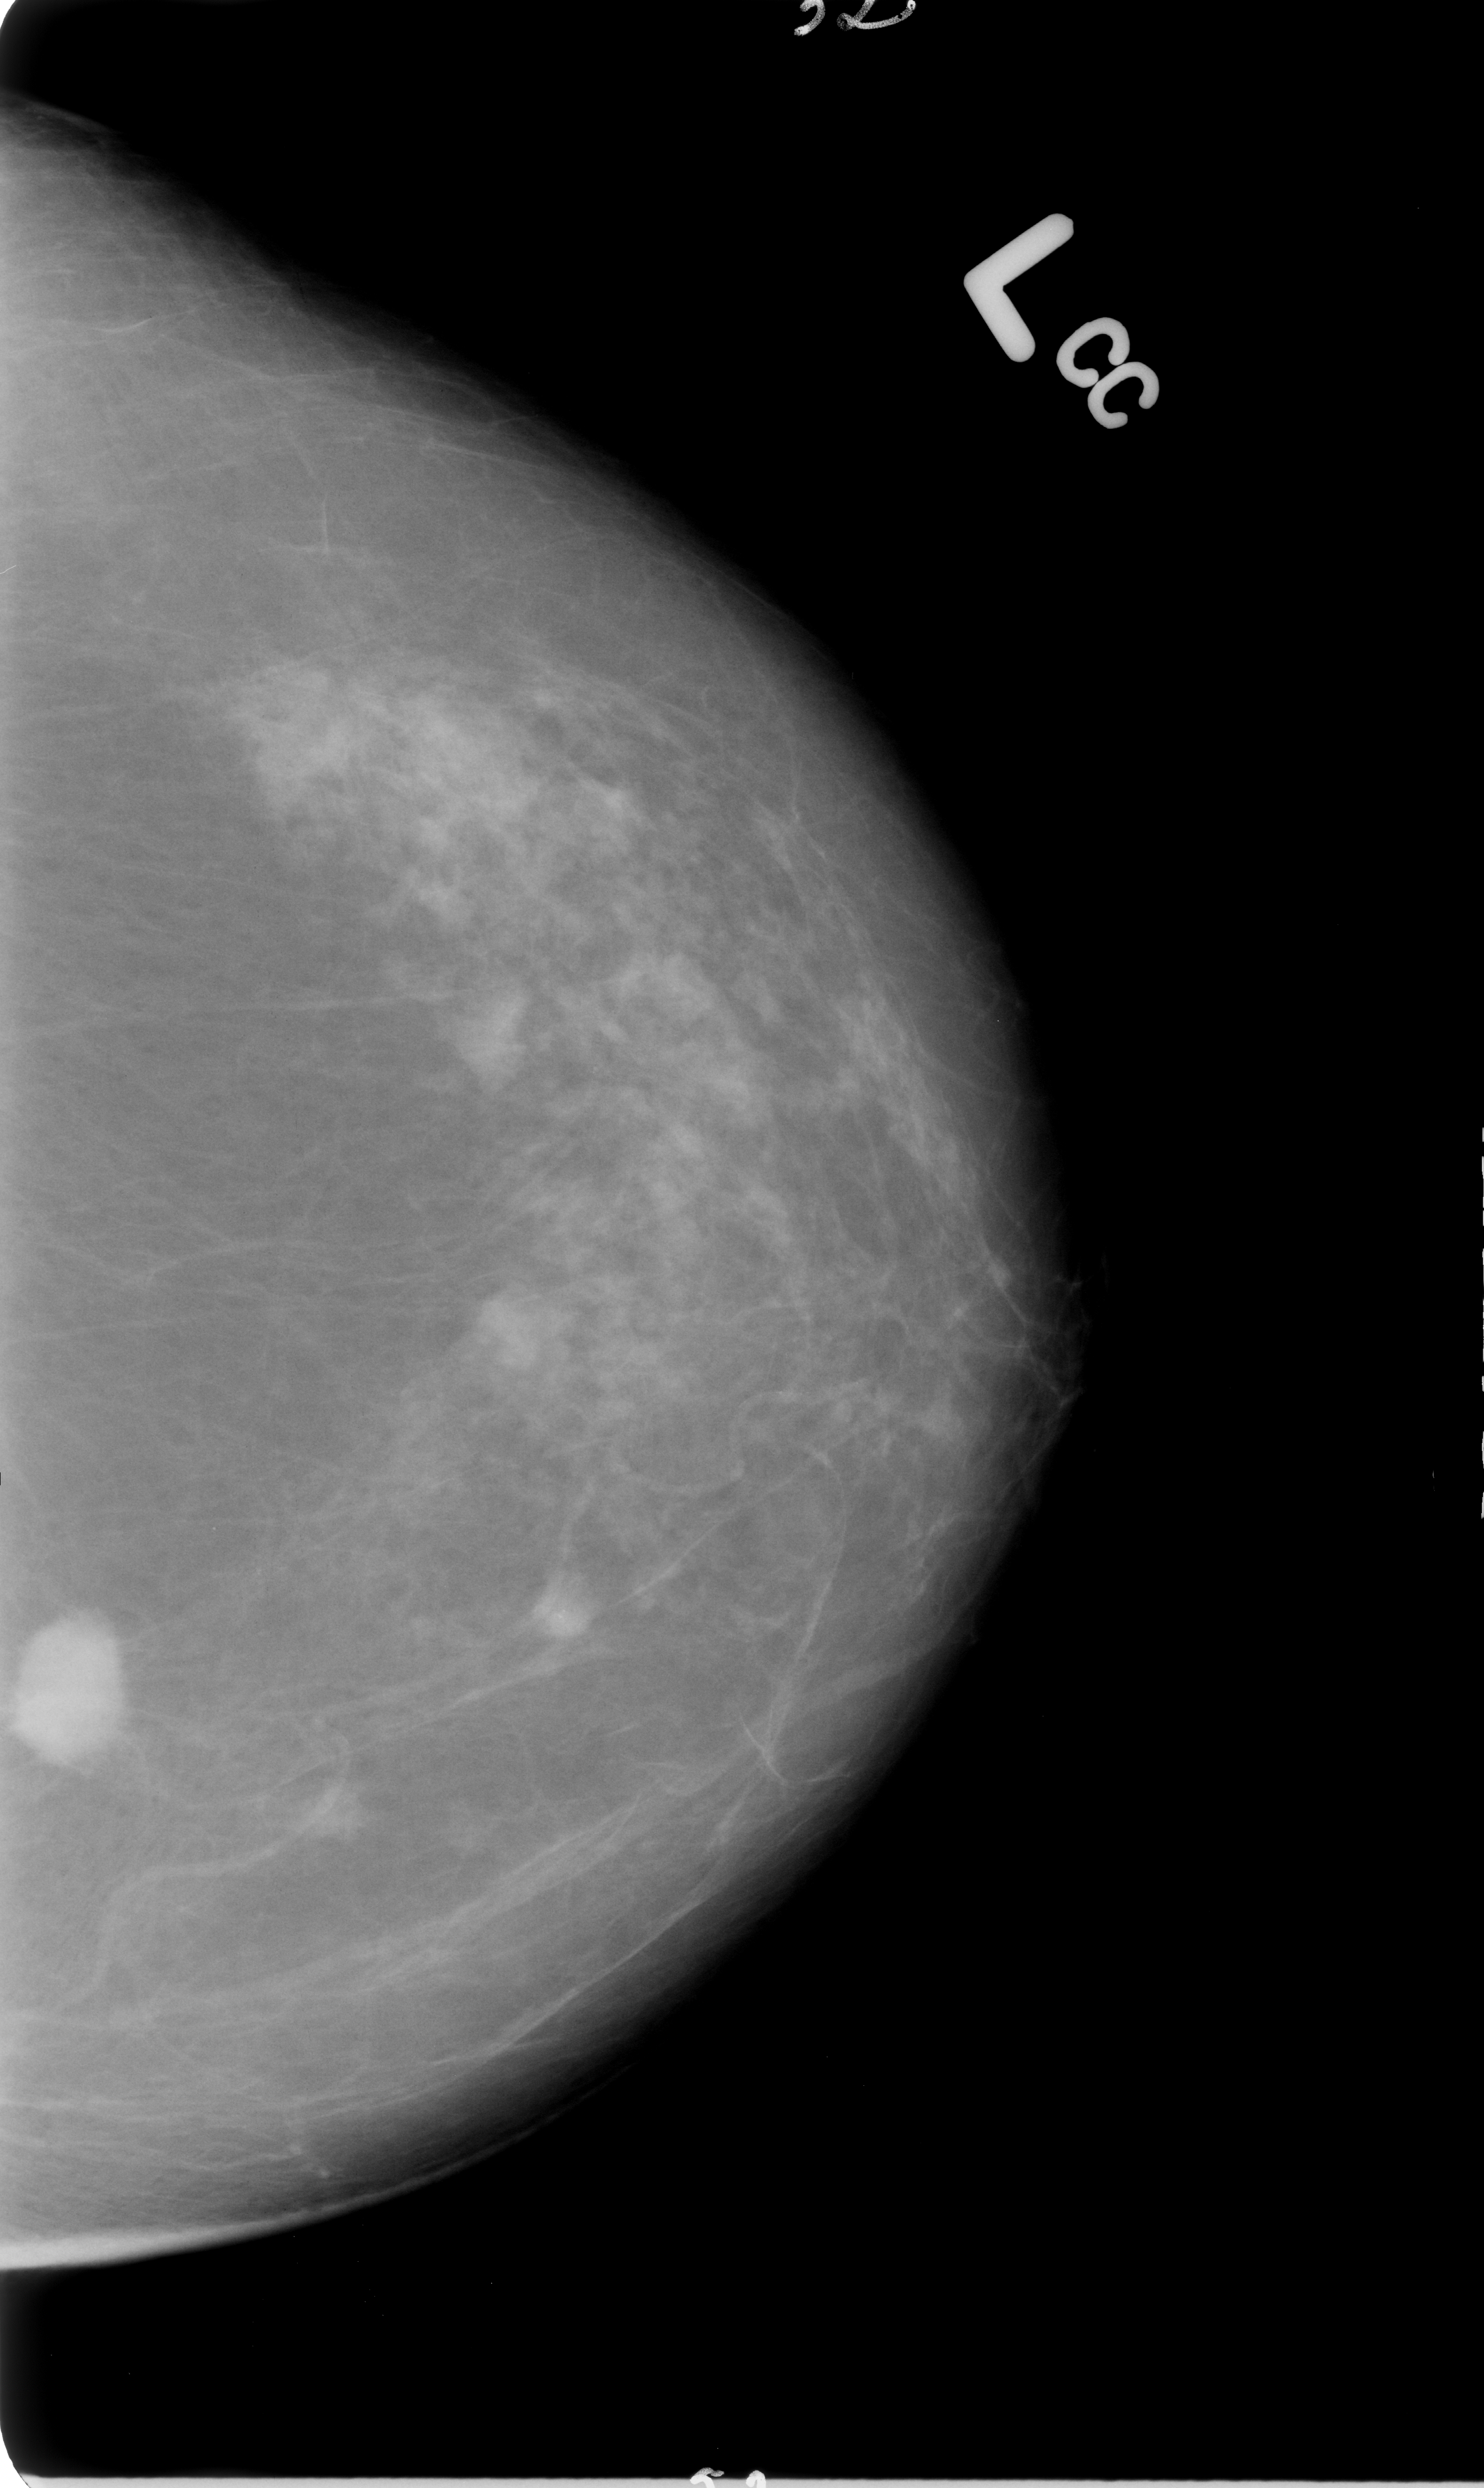
Digitized screen-film mammogram; left breast; craniocaudal (CC) view; breast composition: scattered fibroglandular densities (BI-RADS density category 2 of 4); 1484 × 2488 image matrix.
Marked abnormalities (boxes around the expert regions of interest):
- mass, shape oval, margins spiculated; BI-RADS assessment category 4; pathology (as recorded): malignant: box from (x=0, y=1600) to (x=151, y=1786) px